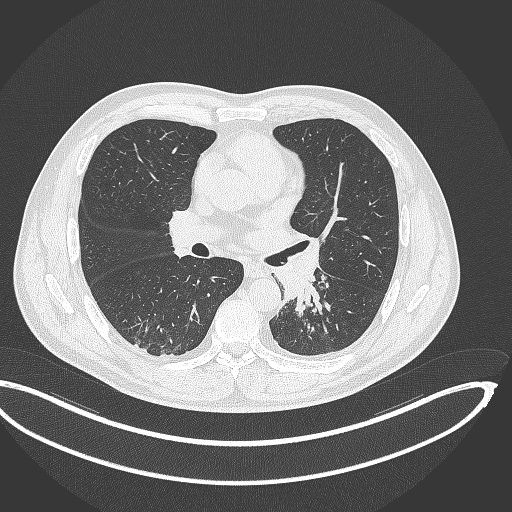
Chest CT, one axial slice; slice 195 of 362 in the series (ordered by position); lung window (W 1500 / L -600 HU); 1 mm slice thickness; 512 × 512 image matrix, field of view 442 × 442 mm. Patient: male, 50 years. Case-level facts recorded for this patient, not image findings: clinical TNM (as recorded): T2a N3 M0.
Structures marked on this image (bounding box drawn by a radiologist):
- lung tumour (recorded histology: squamous cell carcinoma): bounding box (x1, y1, x2, y2) in pixels: (282, 271, 326, 317)